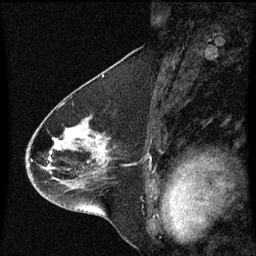
Breast MRI (dynamic contrast-enhanced), one sagittal slice. Slice 34 of 60 in the series (ordered by position). Dynamic contrast-enhanced series, image 2 of 3 at this slice position (ordered by acquisition). 1.5 T. TE 4.2 ms, TR 8.4 ms. 2 mm slice thickness. 256 × 256 image matrix, field of view 200 × 200 mm. Female patient, age 46 years. Case-level facts recorded for this patient, not image findings: setting: breast cancer imaged before/during neoadjuvant chemotherapy; receptor status: HER2-positive.
Structures marked on this image (semi-automatically segmented with operator editing):
- analysis volume of interest (the breast-tissue region the enhancement analysis was run in; not a lesion): bounding box <26,112,116,195> (left, top, right, bottom; pixels)
- tumour enhancement mask (voxels above the 70 % enhancement threshold inside the analysis volume of interest): <55,136,103,149>